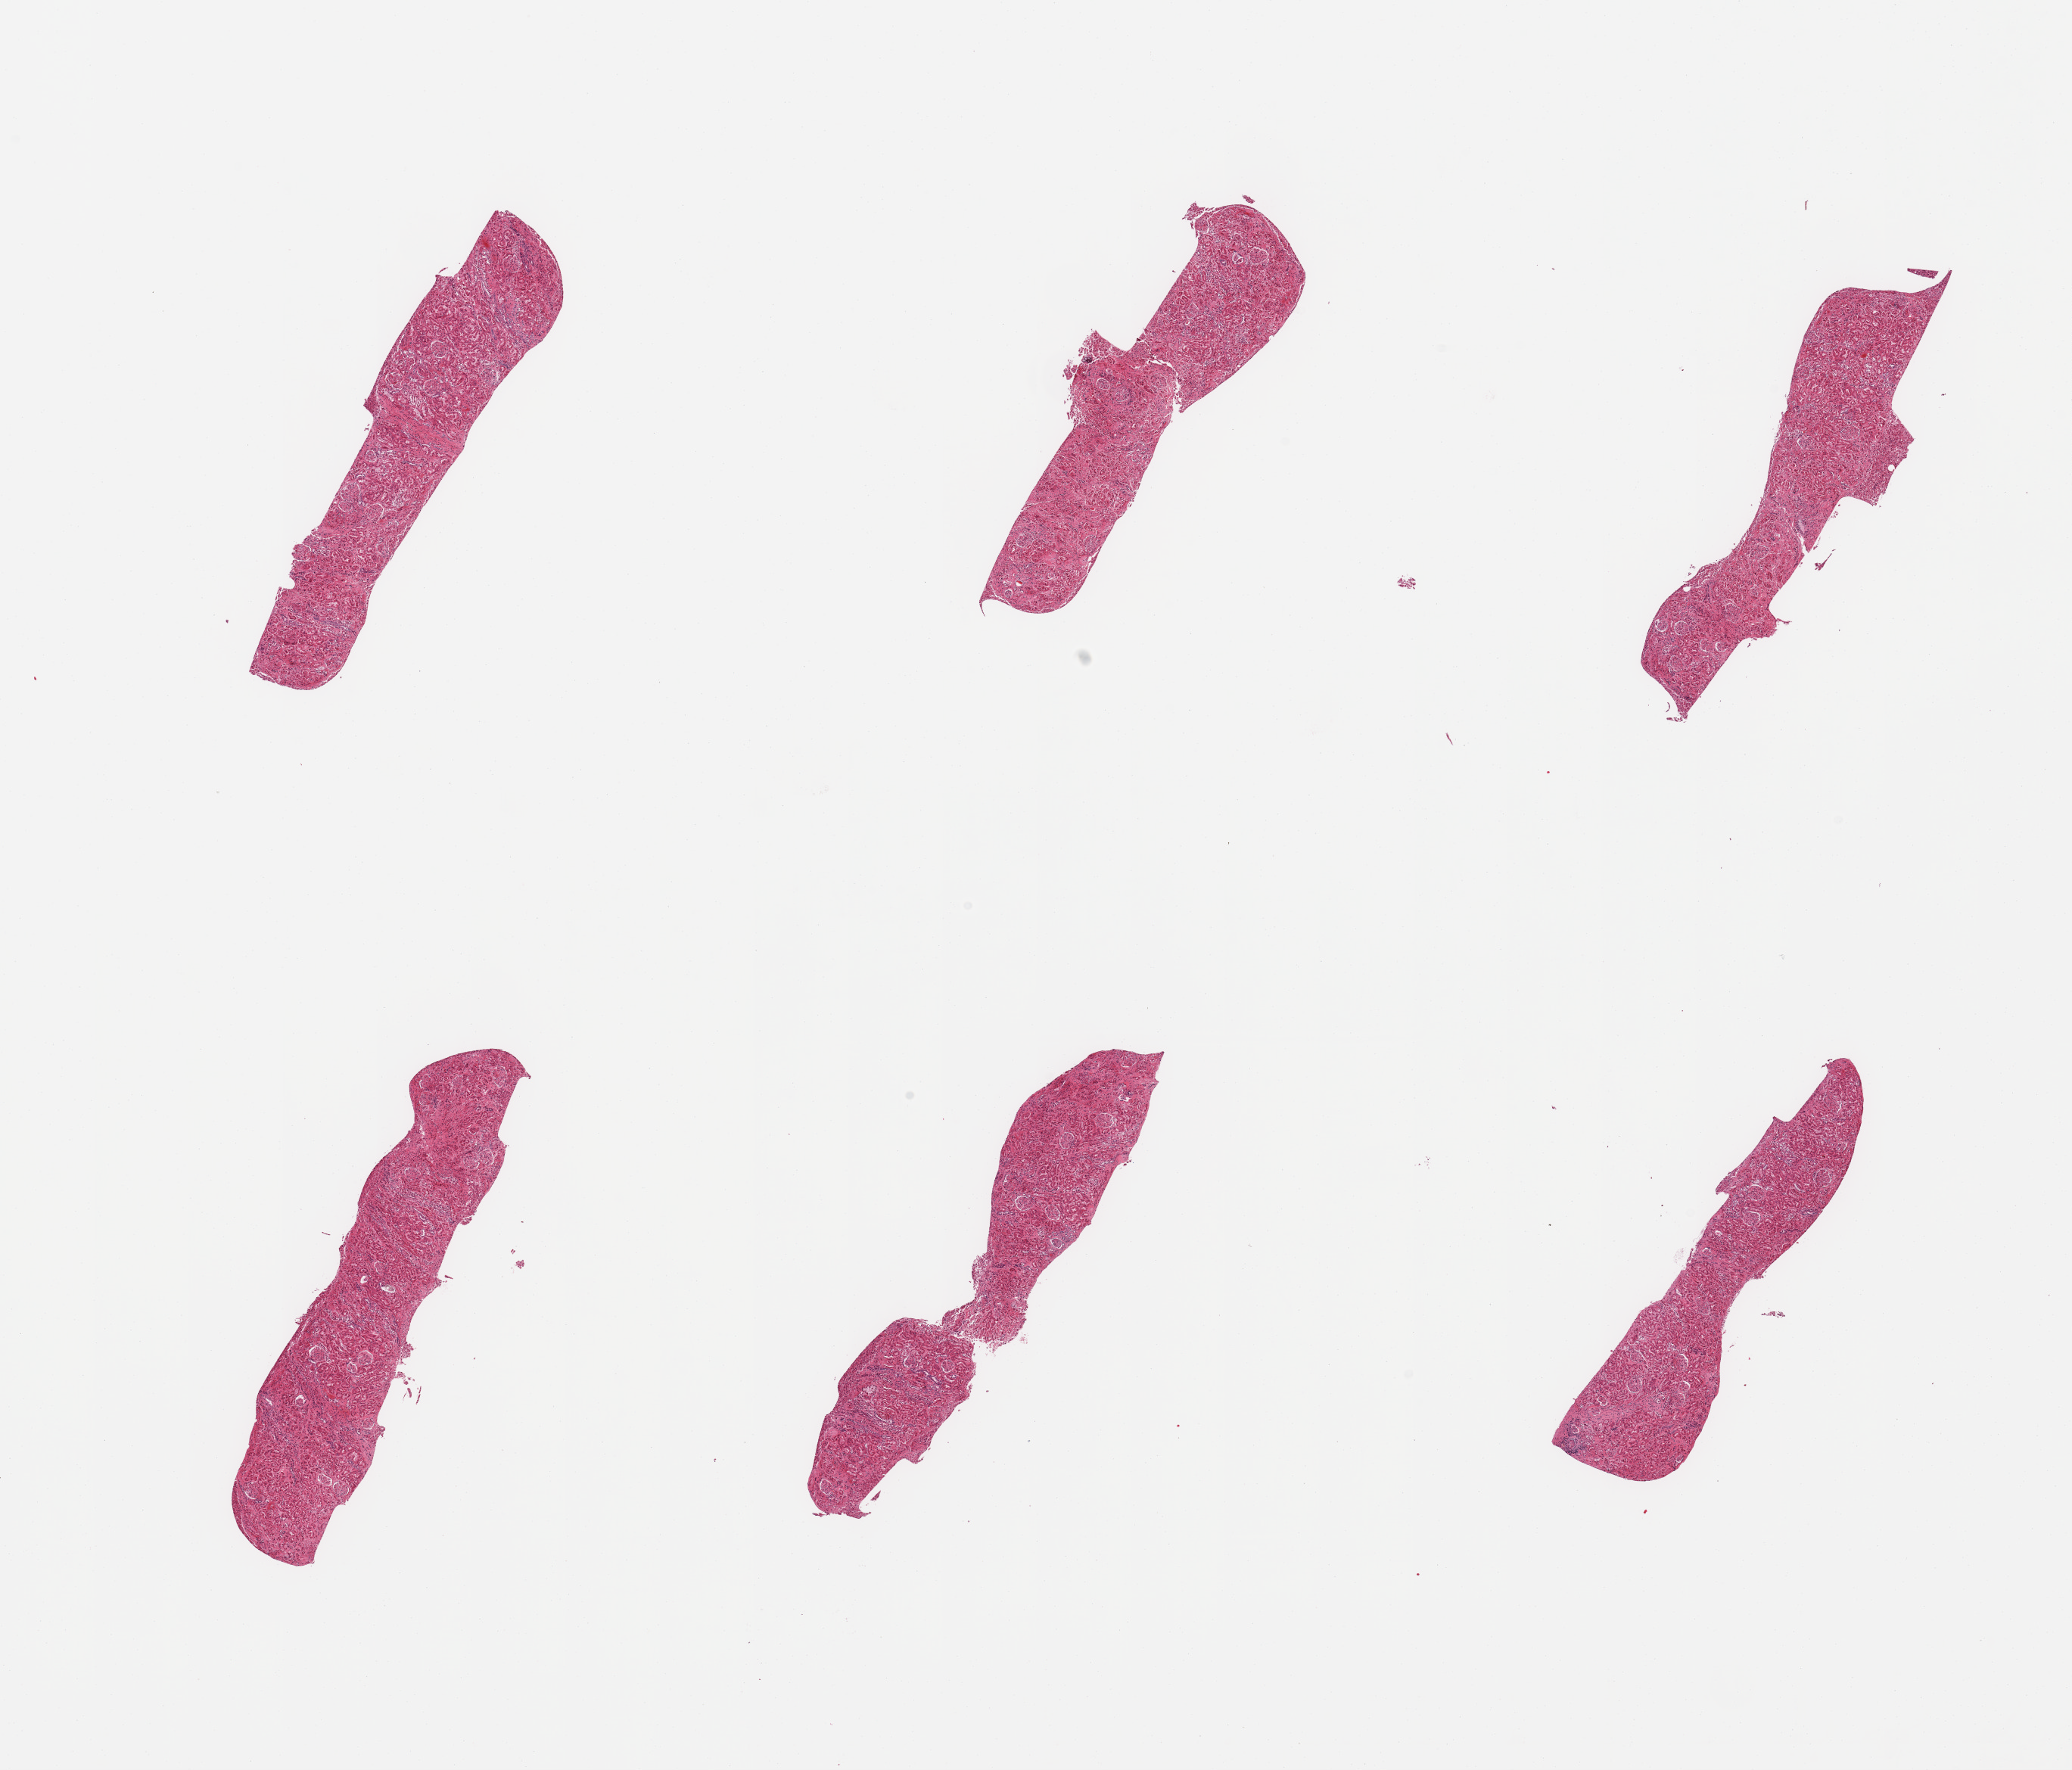
H&E whole-slide image, whole scanned area (about 21.7 x 18.5 mm, slide scanned at 20x) shown as a low-resolution overview. PAXgene-fixed paraffin-embedded (PFPE) section. Target tissue: renal cortex. Tissue donor sample. Donor sex: male.
Reviewer comment on this tissue sample: 6 pieces, tubulars moderately autolyzed.